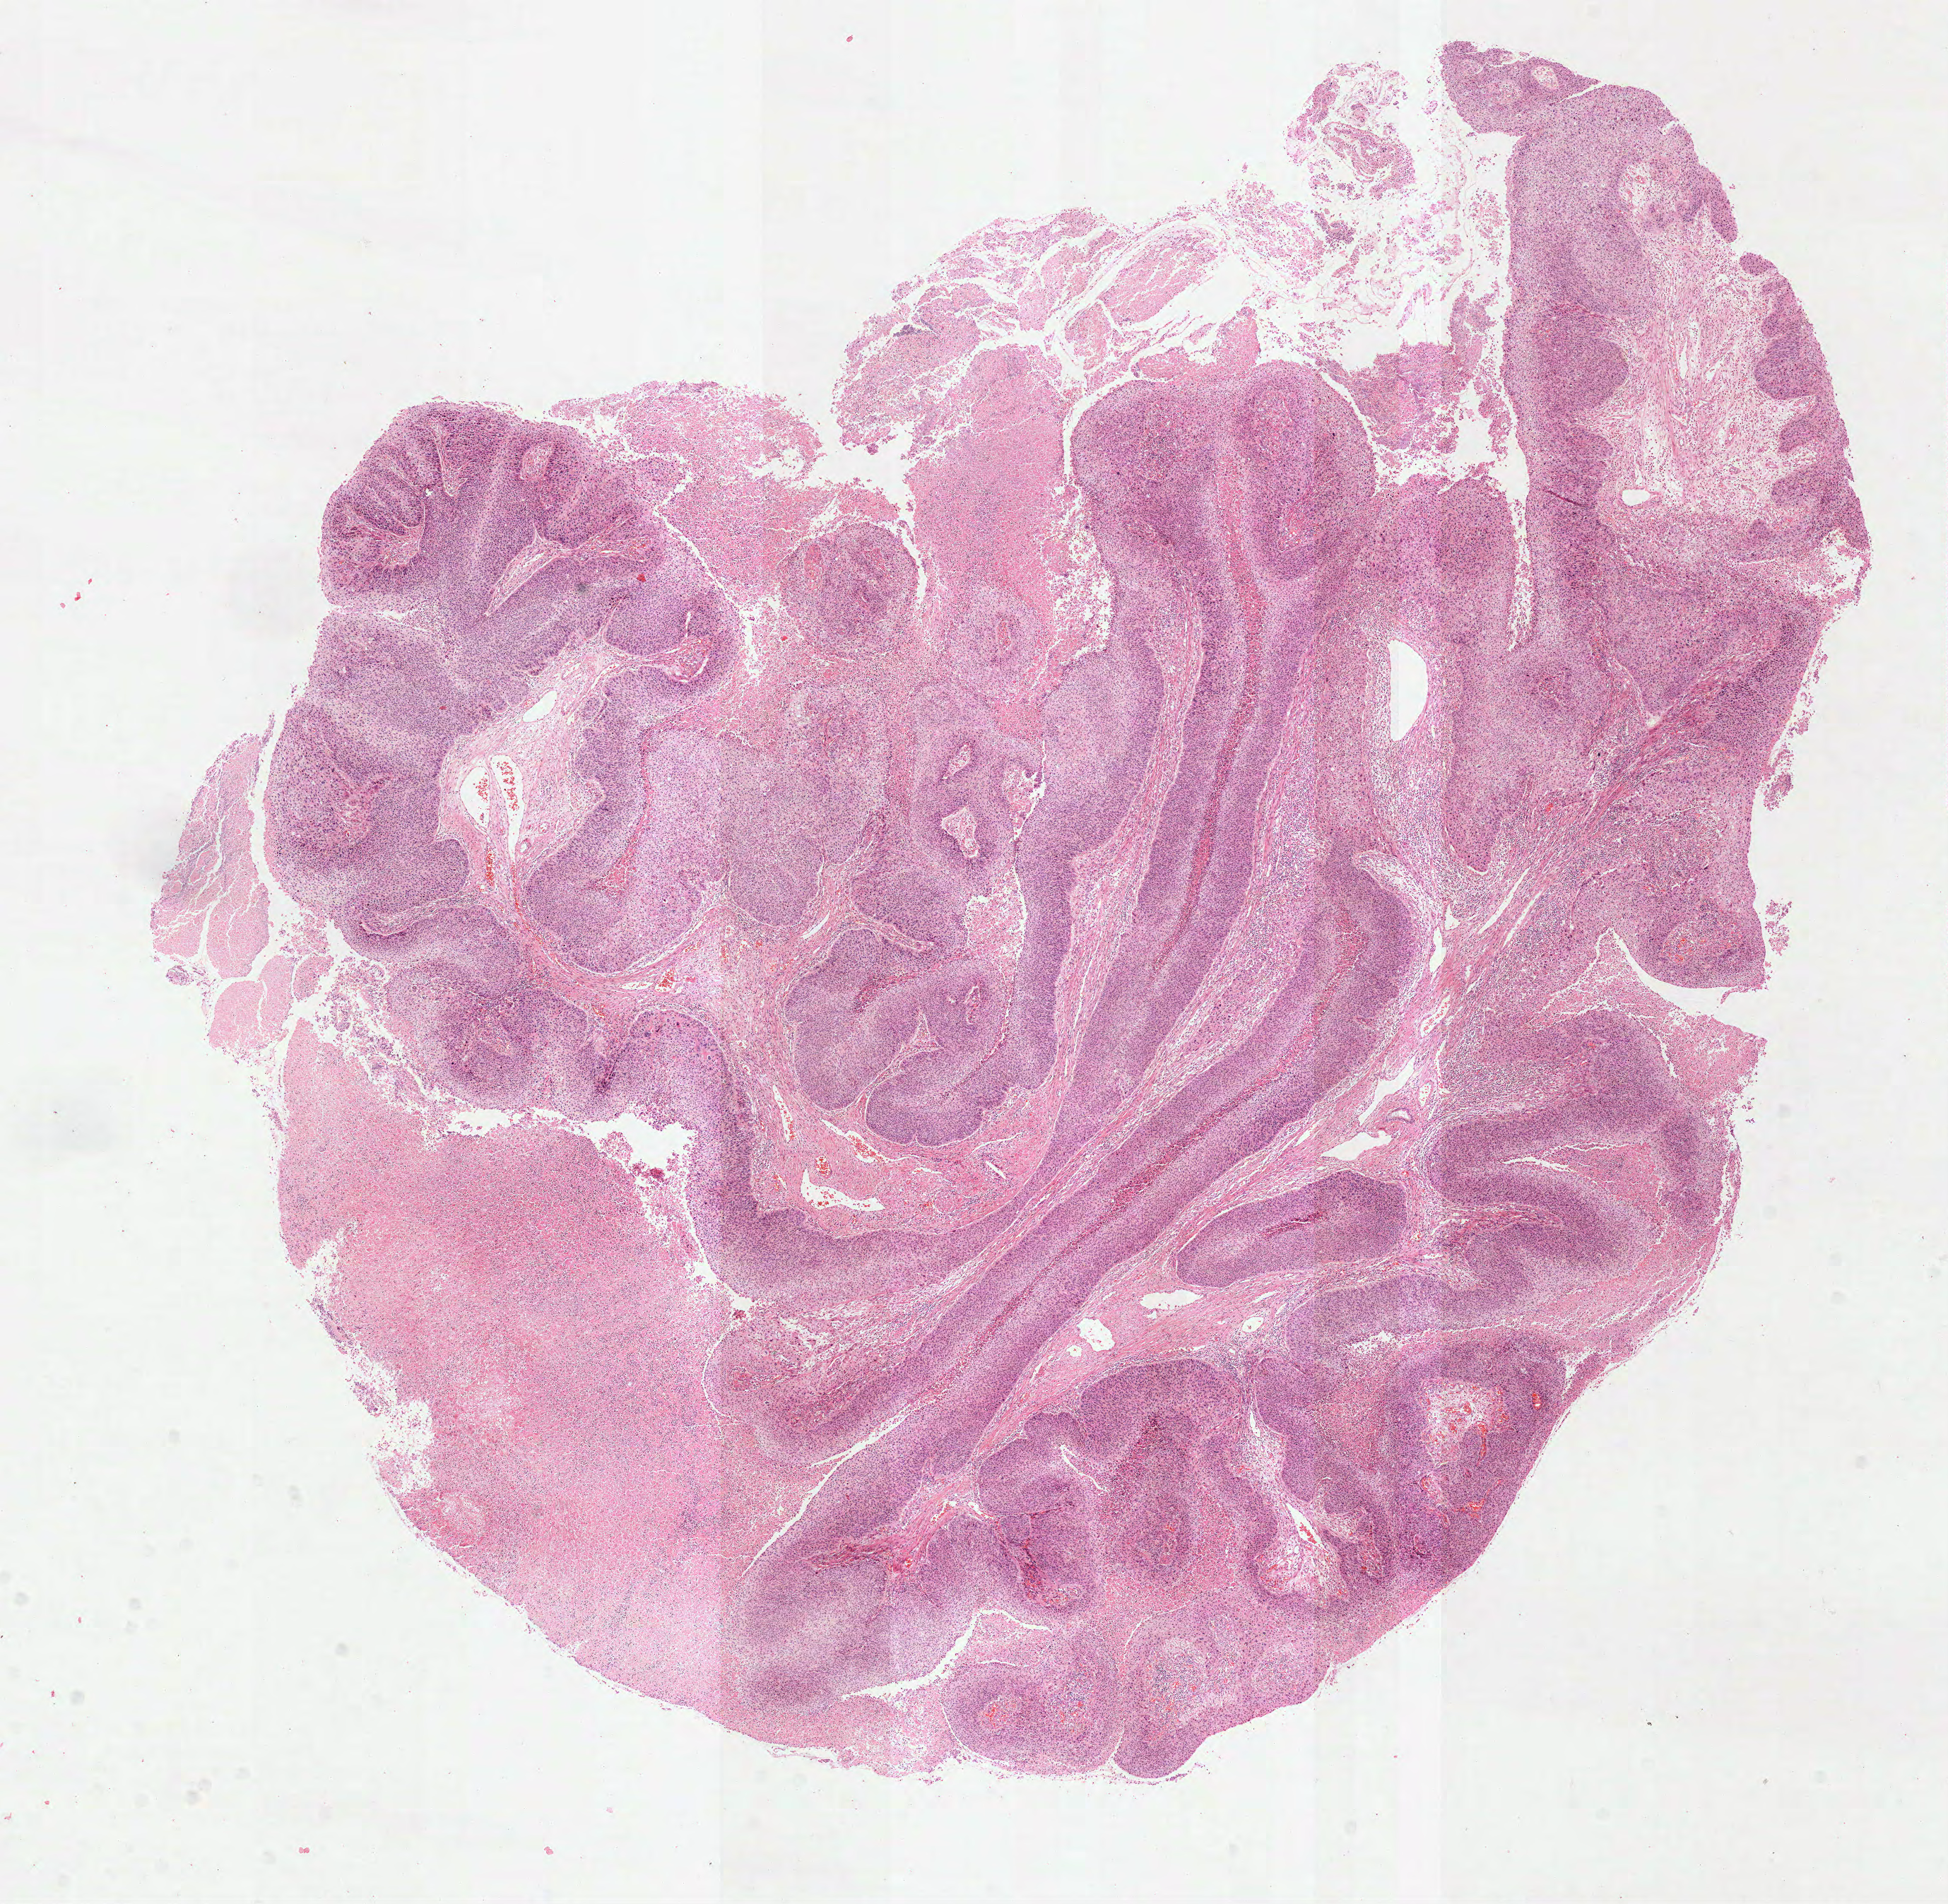
Whole-slide histology image, H&E-stained, low-resolution overview of the scanned area, about 11.1 x 10.9 mm (from a 40x scan), FFPE section, sample: primary tumour, lung. Male, age 66 years at initial diagnosis.
Pathologic diagnosis: Papillary squamous cell carcinoma. AJCC pathologic stage: IA.